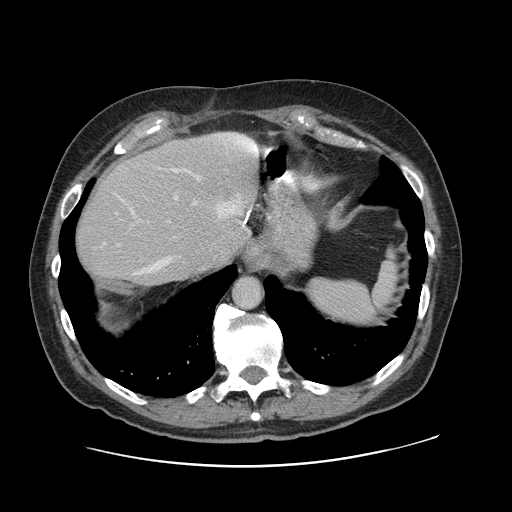
Contrast-enhanced abdominal CT, one axial slice. 120 kVp. Intravenous contrast given. Soft-tissue window (W 400 / L 40 HU). 2.5 mm slice thickness. 512 × 512 image matrix, field of view 402 × 402 mm. Male patient, age 71 years. From the clinical record (not read from this slice): diagnosis: colorectal cancer liver metastases, imaged before liver resection; multiple liver metastases: no; largest metastasis: 3.3 cm.
Annotated regions visible in this slice (outlined manually by an expert reader):
- hepatic veins: bounding box [x1, y1, x2, y2] px = [135, 178, 250, 274]
- liver: [75, 133, 259, 287]
- planned liver remnant (the part of the liver to remain after resection): [75, 157, 232, 287]